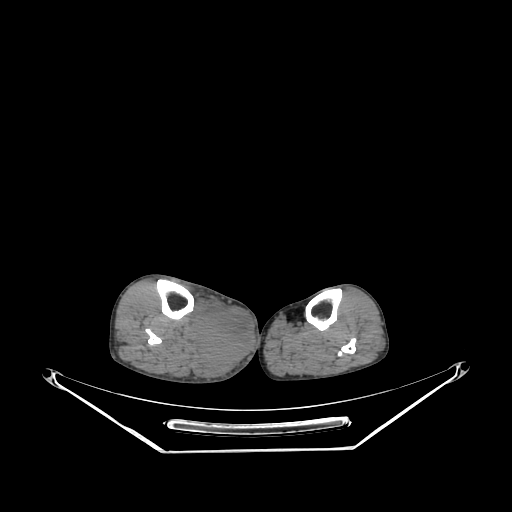
CT of an extremity soft-tissue mass (from a PET/CT study), one axial slice; position 134 of 267 along the scan axis; 140 kVp; soft-tissue window (W 400 / L 40 HU); 3.75 mm slice thickness; 512 × 512 image matrix, field of view 500 × 500 mm. Male patient. From the clinical record (not read from this slice): histological type: pleiomorphic liposarcoma; grade: high; site of the primary tumour: right calf.
Structures marked on this image (expert contour drawn on MRI and transferred to this co-registered scan by the dataset authors):
- gross tumour volume including surrounding oedema: bounding box (x1, y1, x2, y2) in pixels: (196, 299, 254, 378)
- gross tumour volume (mass): (196, 306, 254, 364)